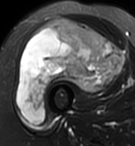
MRI of an extremity soft-tissue mass, one axial slice. Slice 50 of 95 in the series (ordered by position). T2-weighted fat-saturated. MR volume resampled by the dataset authors to the PET/CT grid (not the native acquisition matrix). 3.27 mm slice thickness. 135 × 146 image matrix, field of view 132 × 143 mm. Female patient. Case-level facts recorded for this patient, not image findings: histological type: pleiomorphic undifferentiated sarcoma; grade: high; site of the primary tumour: right quadricep.
Annotated regions visible in this slice (expert contour drawn on MRI and transferred to this co-registered scan by the dataset authors):
- gross tumour volume including surrounding oedema: box from (x=16, y=18) to (x=125, y=124) px
- gross tumour volume (mass): (x=16, y=18)–(x=125, y=124)